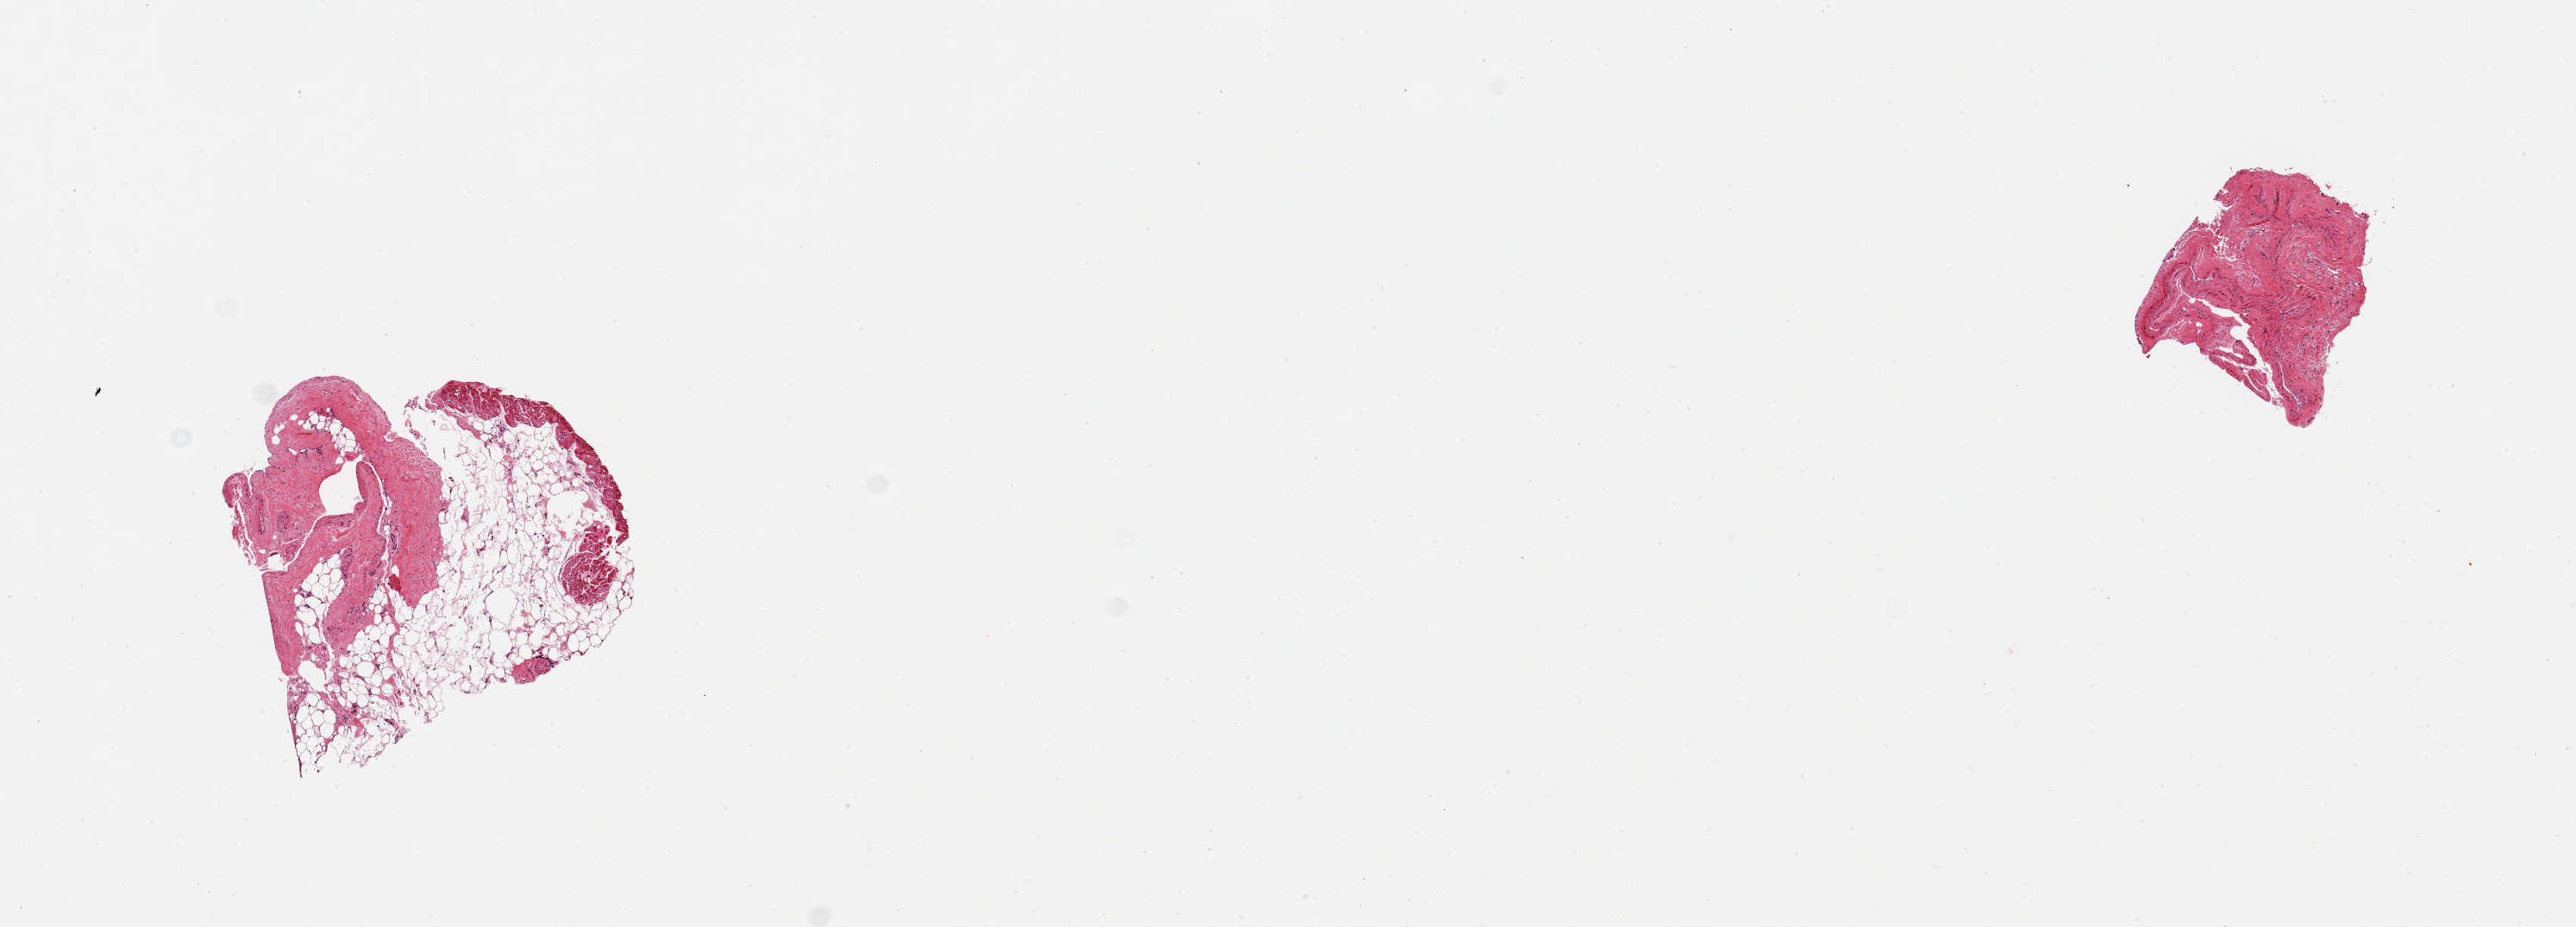
Whole-slide image, H&E stain, brightfield, whole scanned area (about 11.8 x 4.3 mm, from a 20x scan) shown as a low-resolution overview, PAXgene-fixed paraffin-embedded (PFPE) section, section of coronary artery (target tissue), donor tissue sample. Donor: female.
Pathologist's review note for this sample: 2 pieces, no artery, venous/adipose/connective tissues.